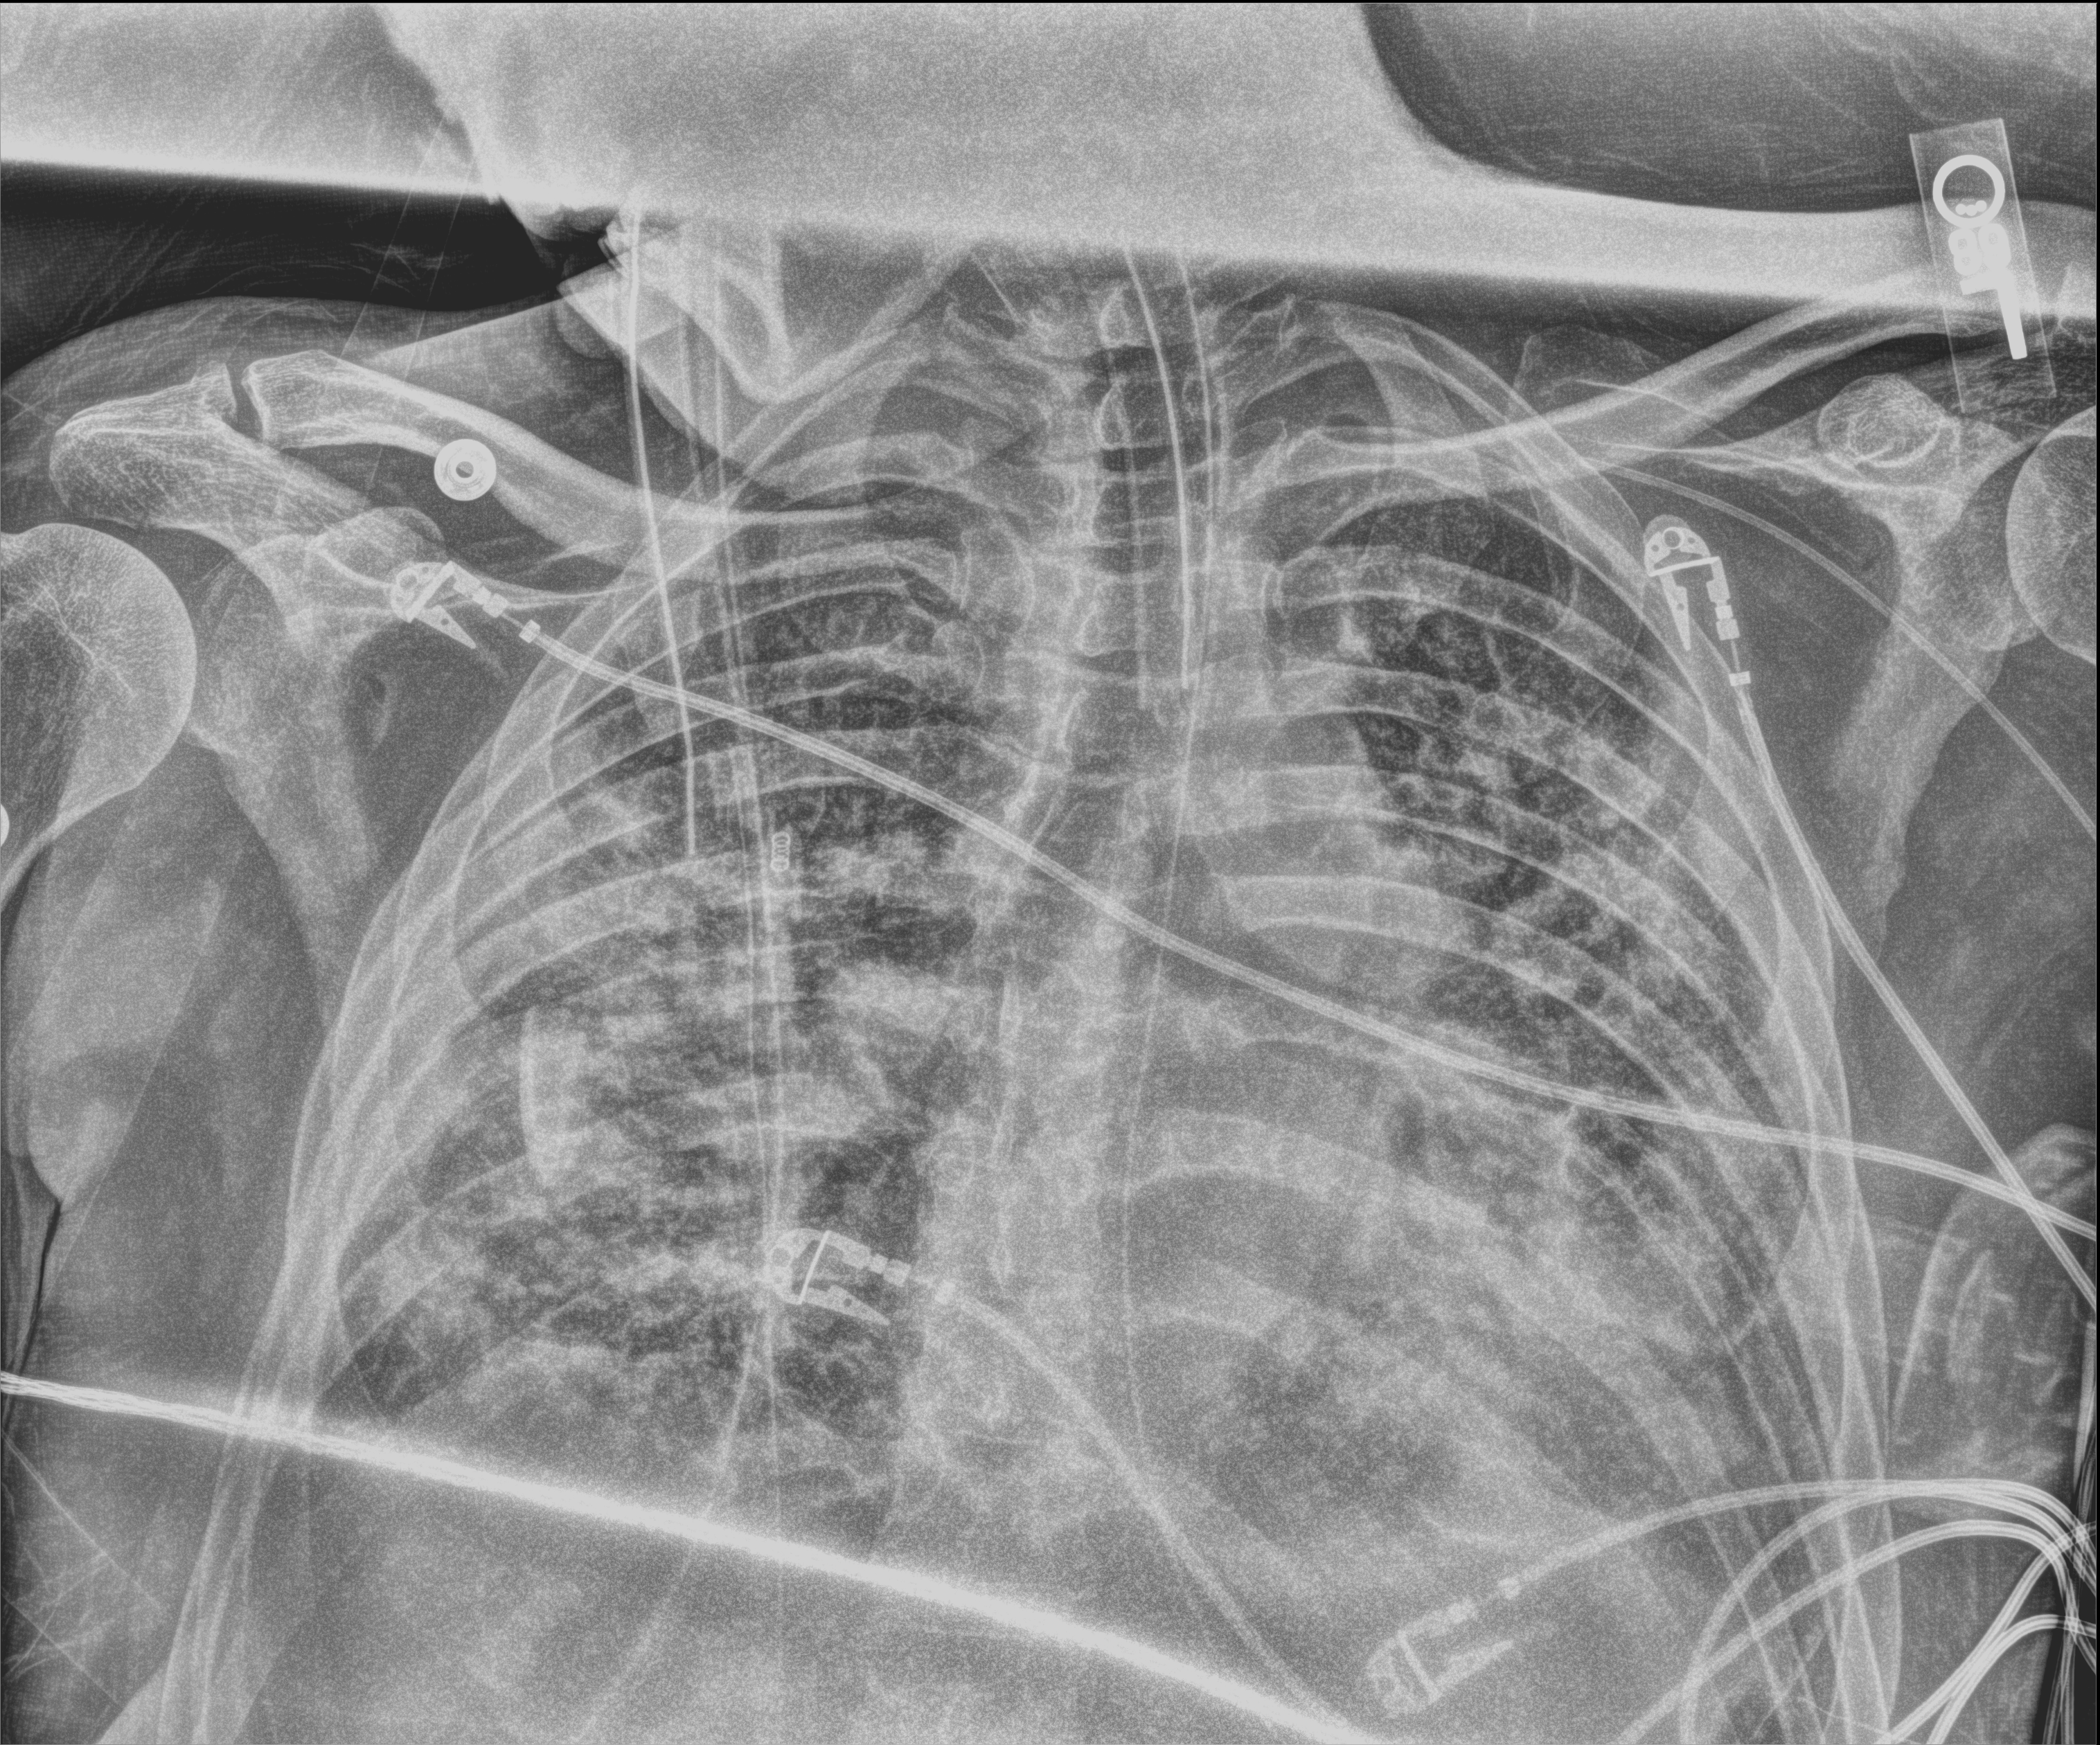
Portable chest radiograph. Patient hospitalised with COVID-19; male, aged 18–59 years.
Admission-level facts for this patient (not findings on this image; timing relative to this image not recorded): other chronic lung disease (admission record): no; length of hospital stay: 75 days; mechanically ventilated during this hospital stay: yes.